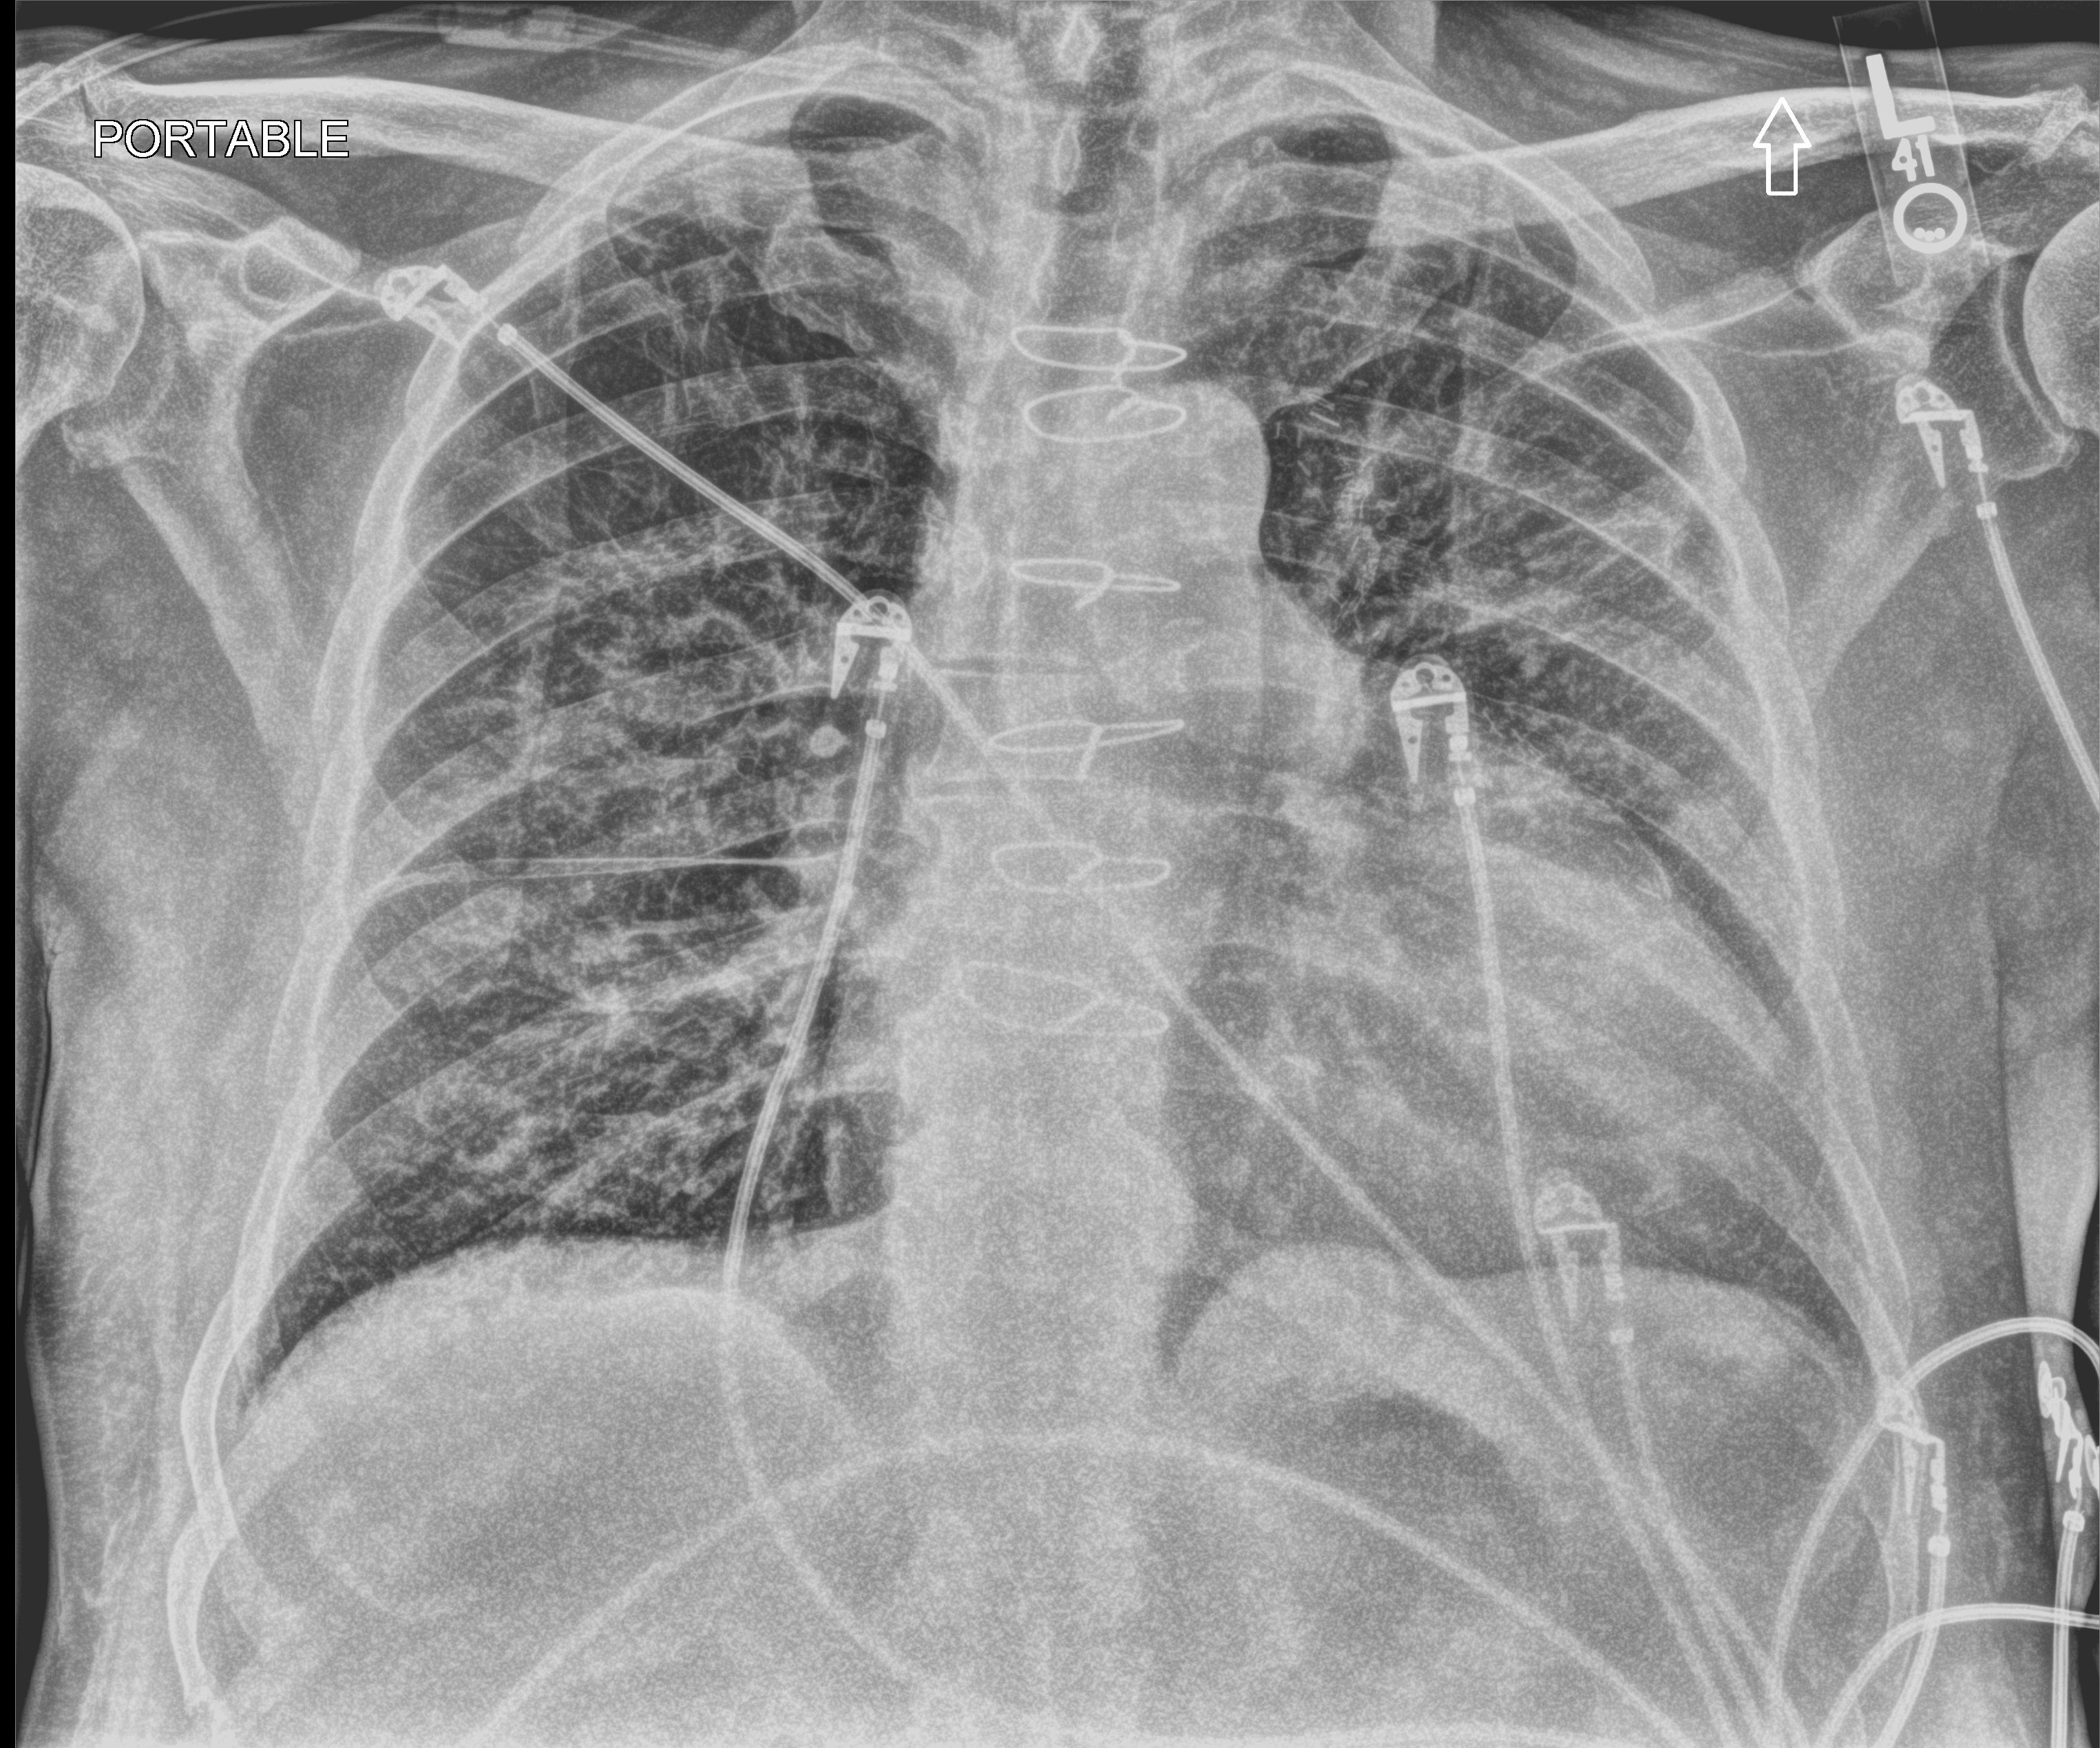
Portable chest radiograph; anteroposterior (AP) projection. Male patient hospitalised with COVID-19, age 75–90 years.
Admission-level facts for this patient (not findings on this image; timing relative to this image not recorded): COPD (admission record): yes.